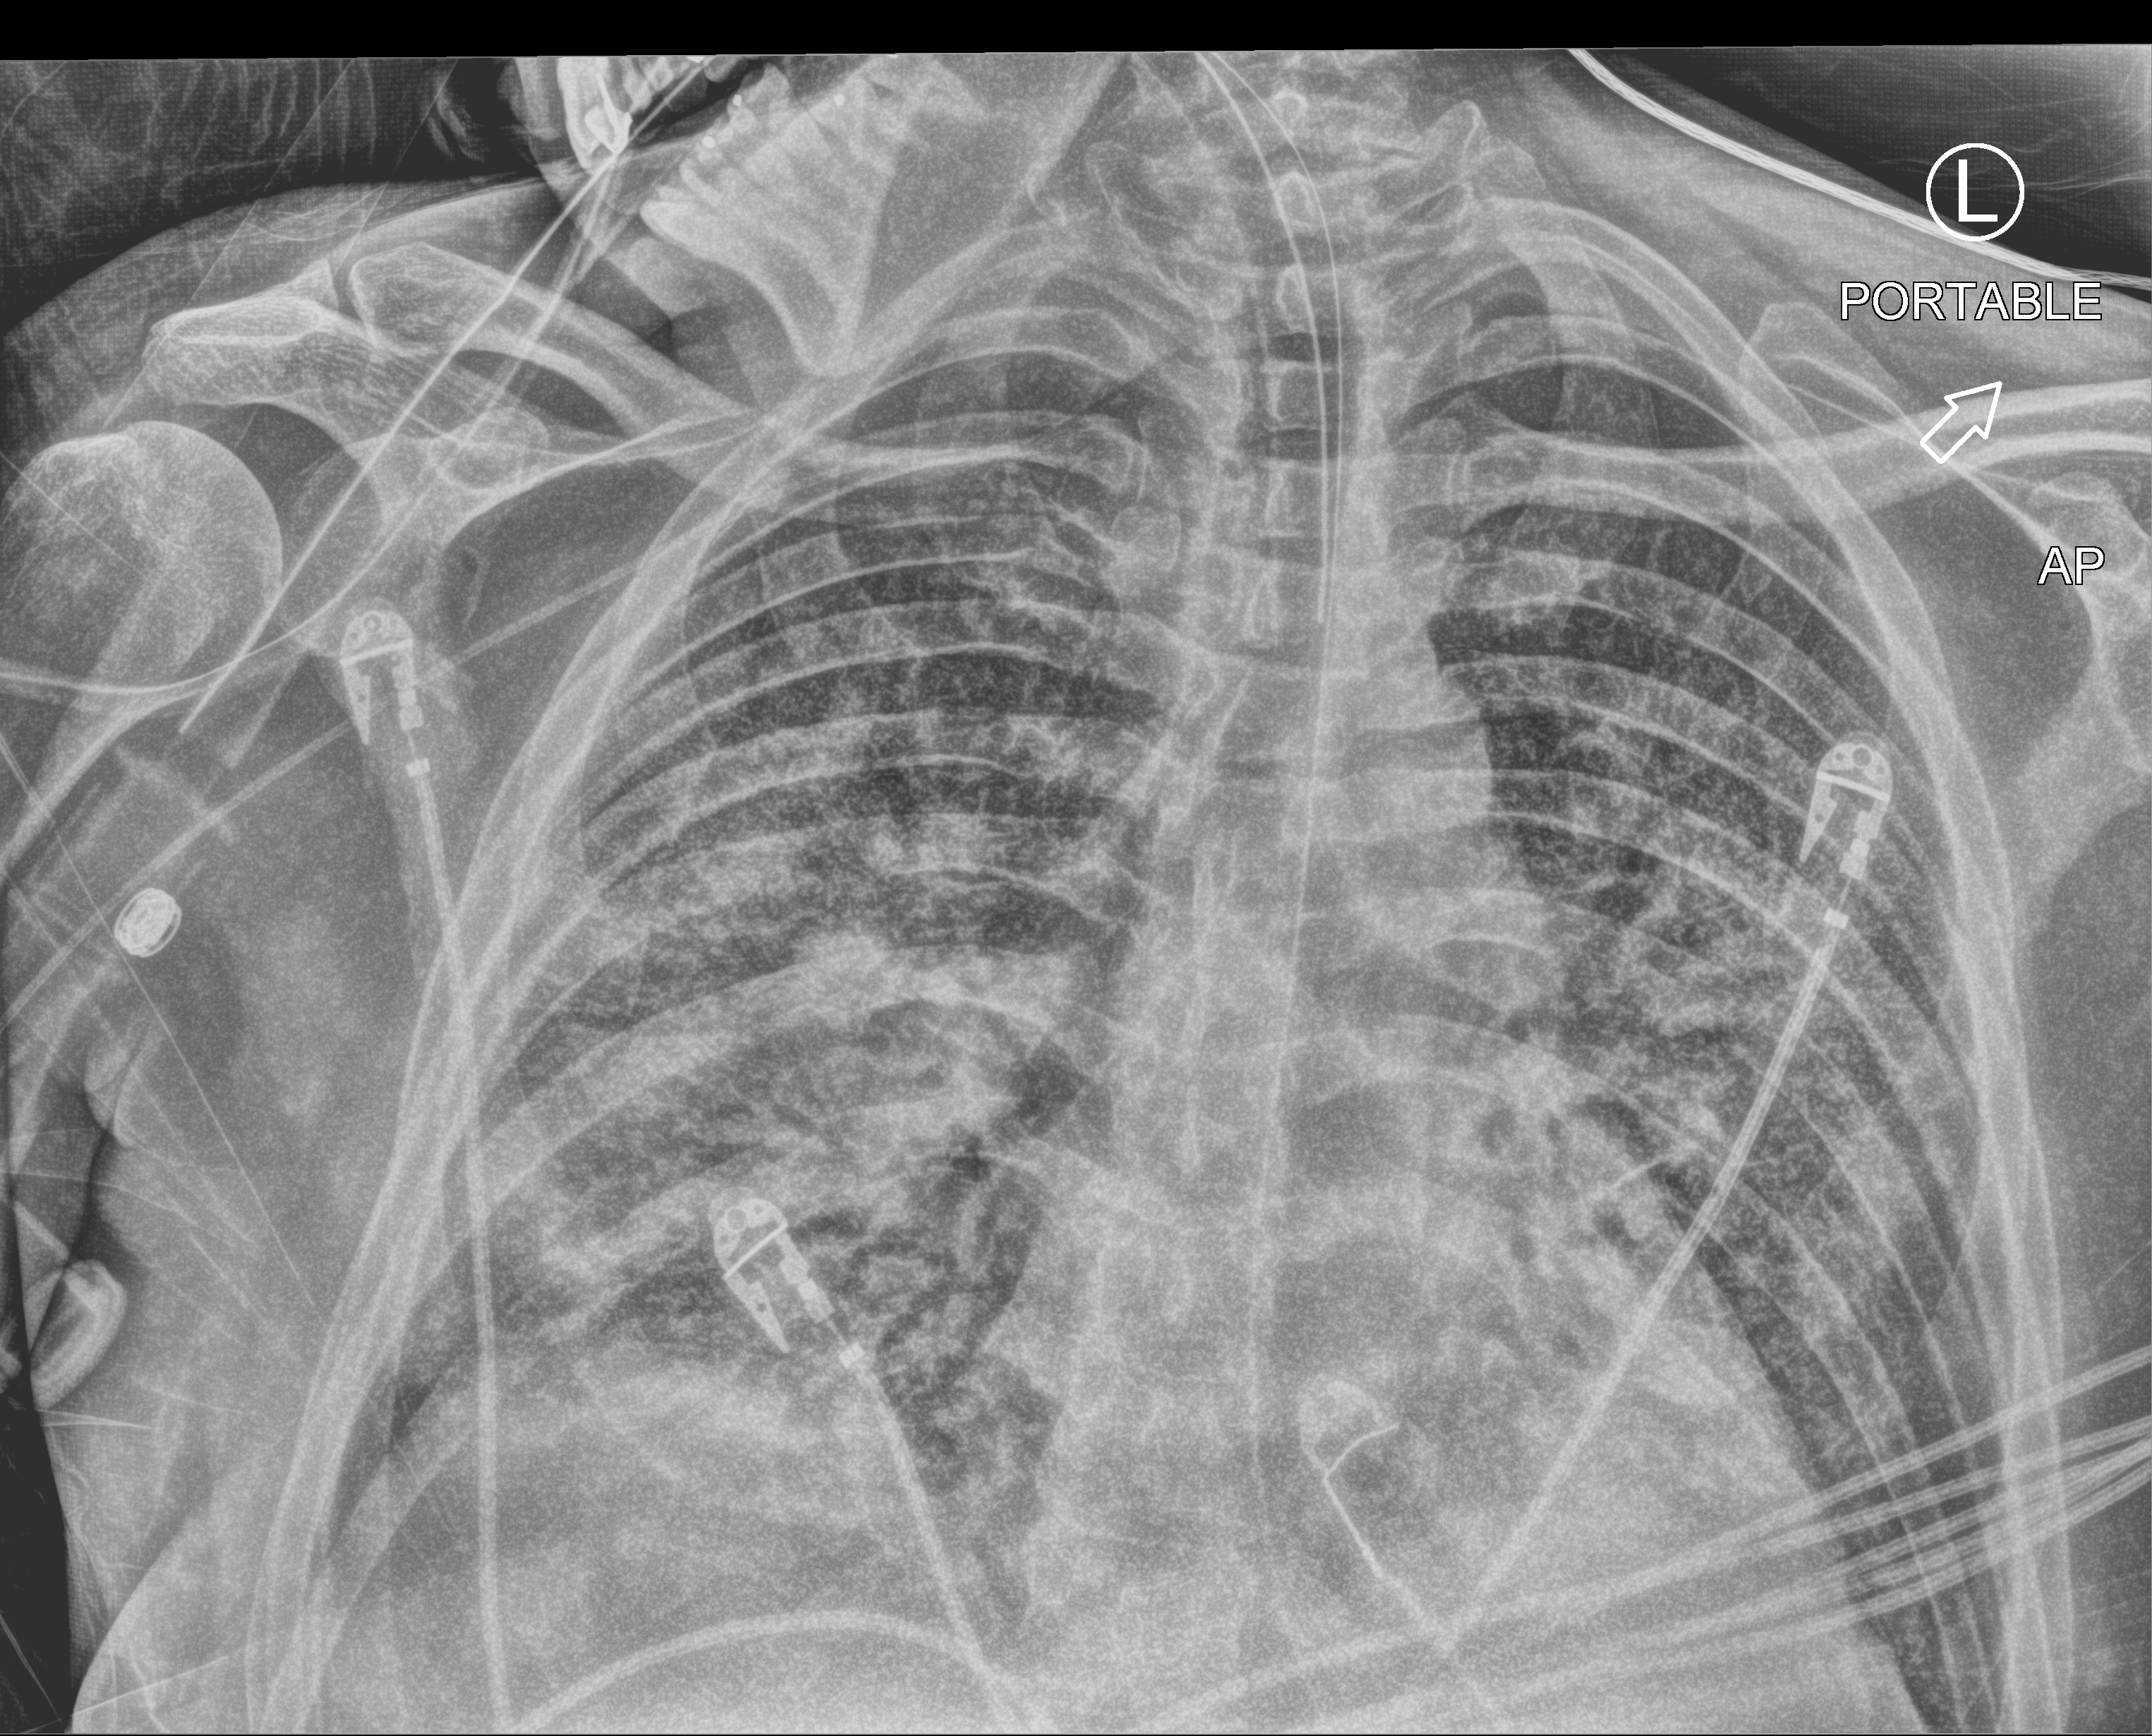
Chest X-ray (portable), anteroposterior (AP) projection. Patient hospitalised with COVID-19; male, aged 18–59 years.
Hospital-stay facts (about this admission, not read from this image; timing relative to this image not recorded): mechanically ventilated during this hospital stay: yes; admitted to intensive care during this hospital stay: yes.